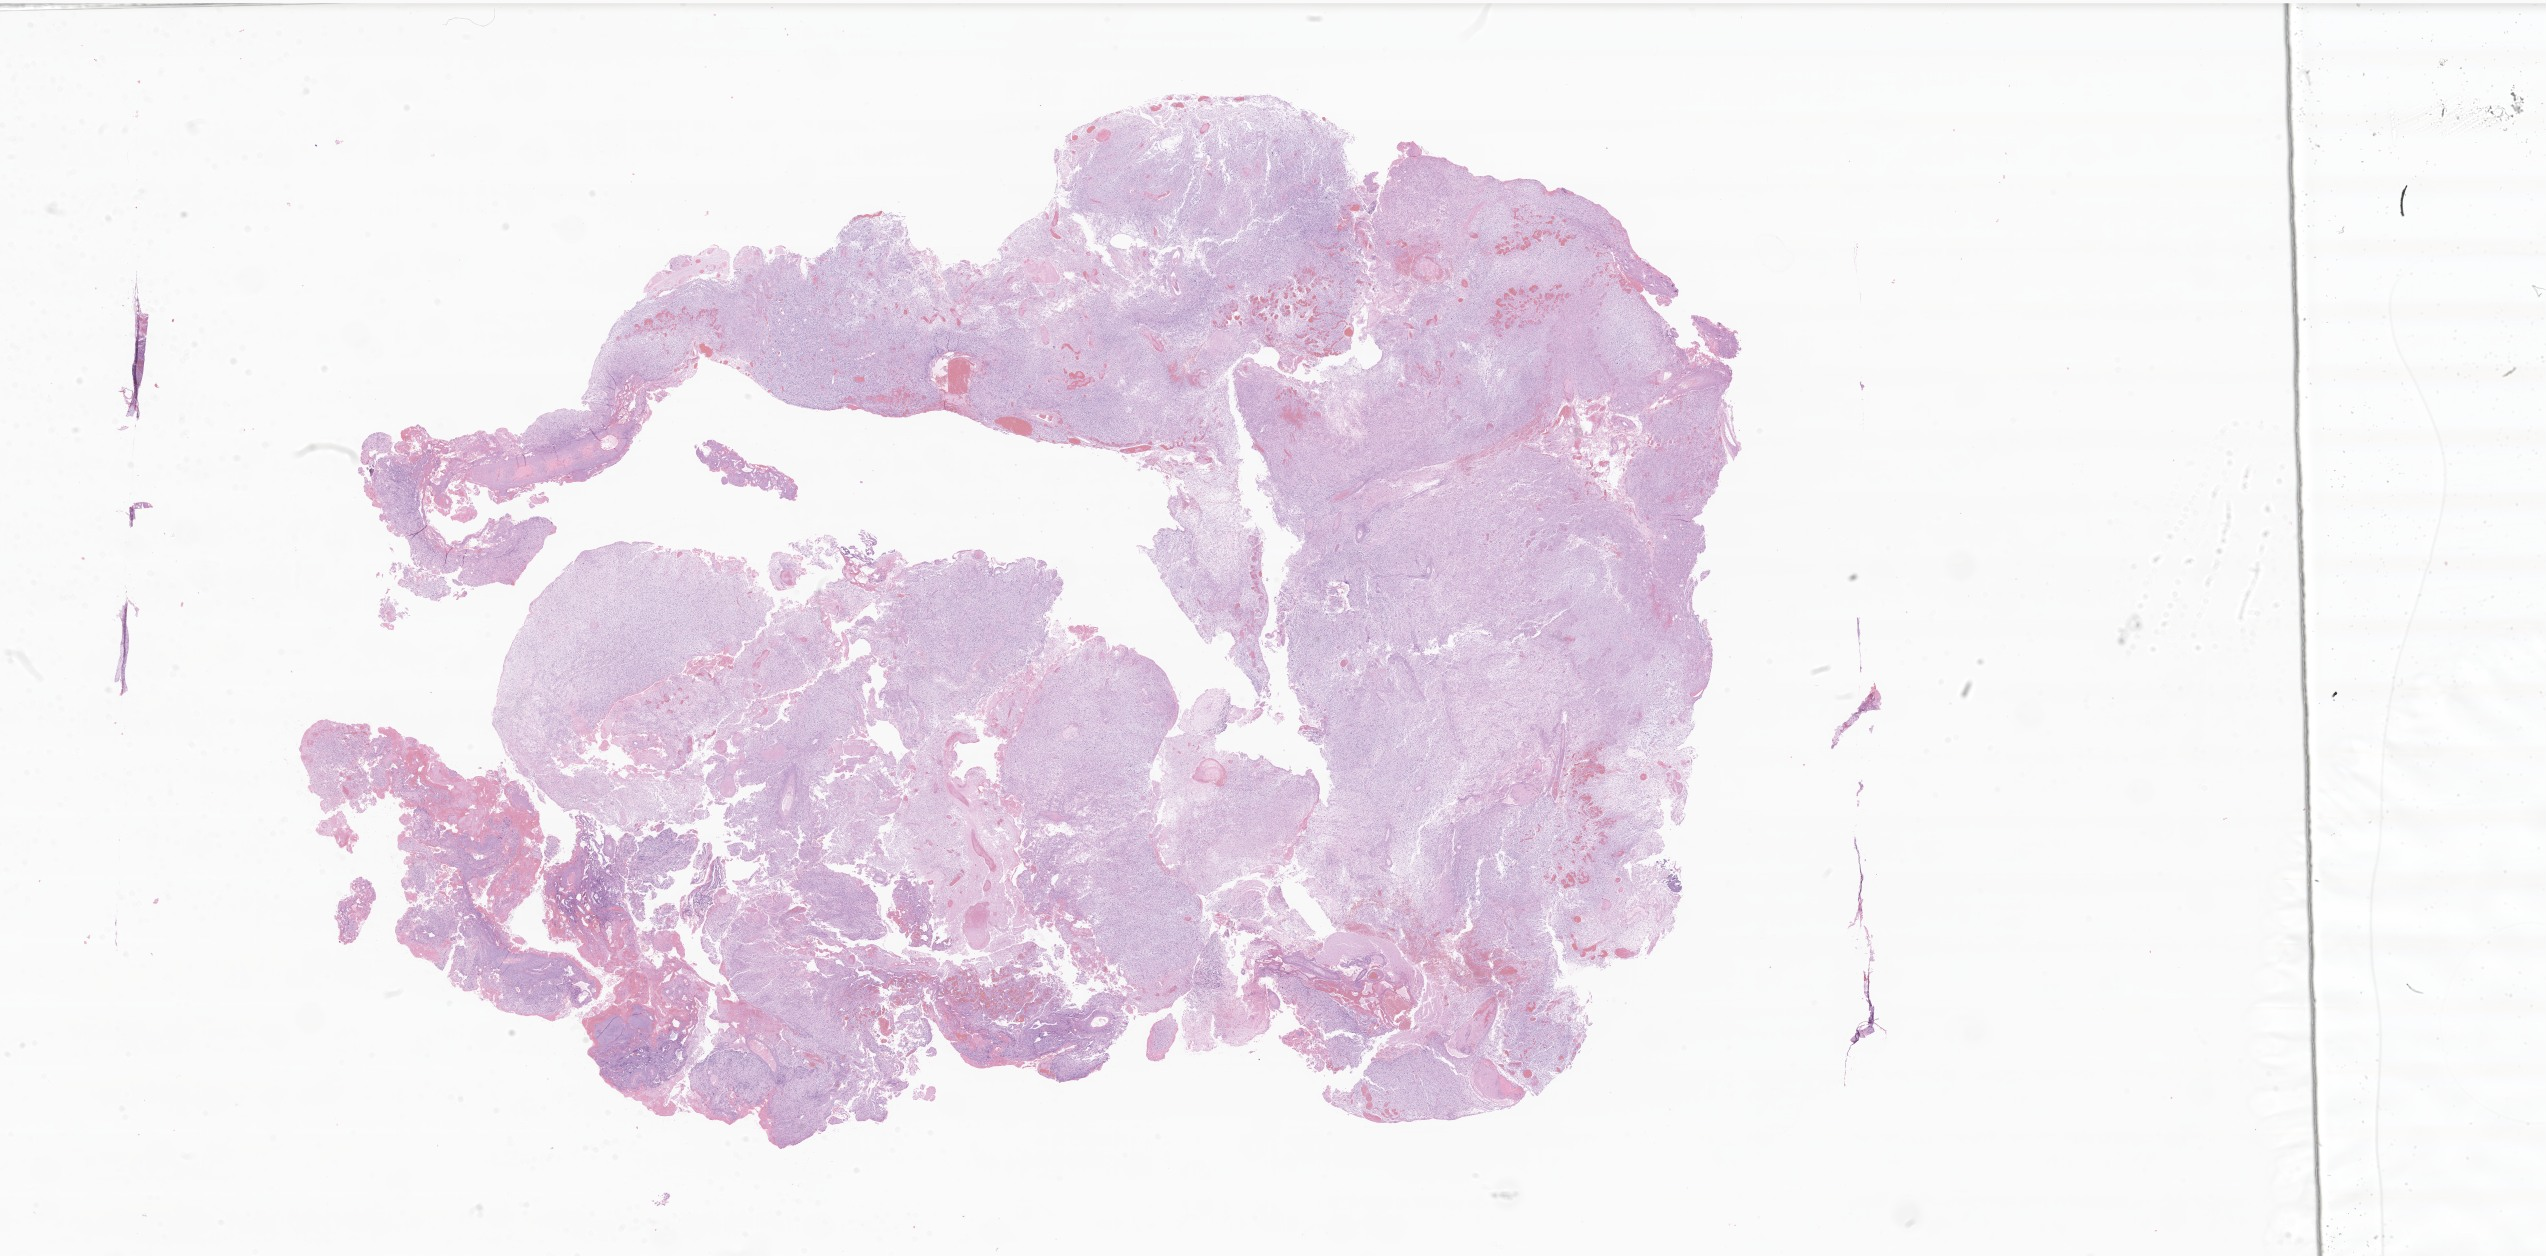
Digitized H&E-stained section of tumor tissue from the brain, whole scanned area (about 42.9 x 21.2 mm) shown as a low-resolution overview. Formalin-fixed, paraffin-embedded (FFPE) tissue. Patient male; age 71 months (5 years 11 months).
• diagnosis (ICD-O-3 morphology term): Glioblastoma, NOS